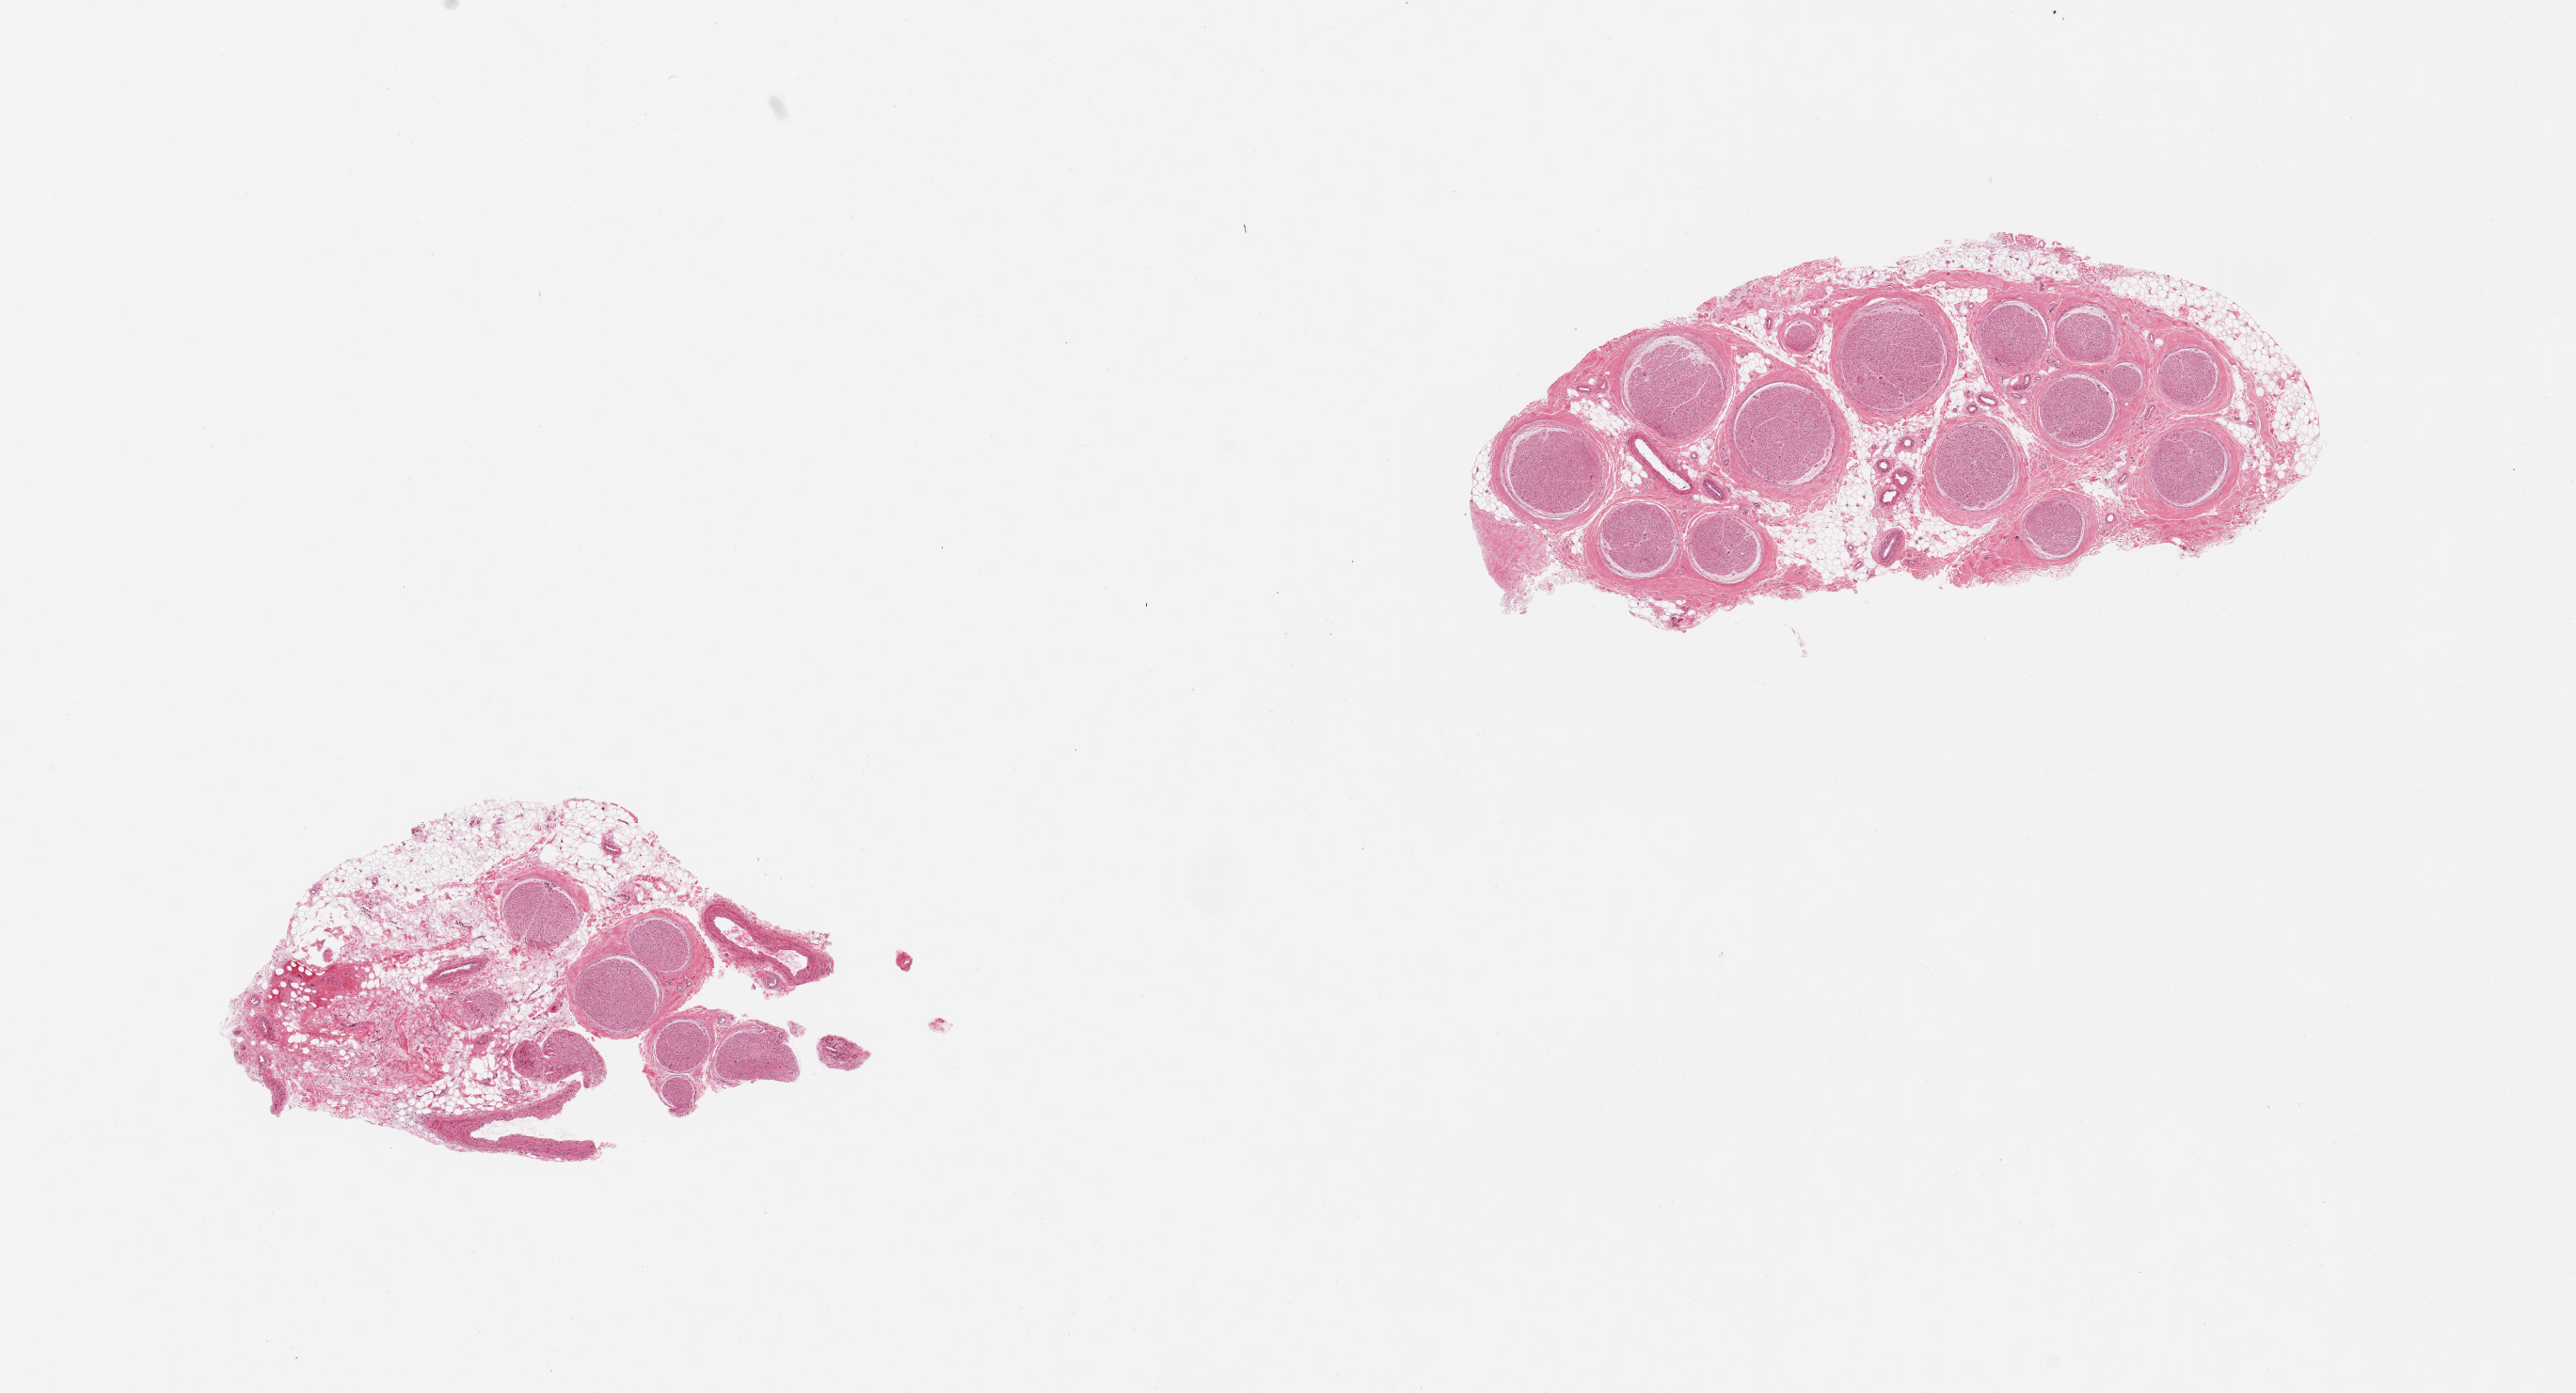
Hematoxylin and eosin (H&E) whole-slide image — whole scanned area (about 21.7 x 11.7 mm) shown as a low-resolution overview, PAXgene-fixed paraffin-embedded (PFPE) section, target tissue: tibial nerve, tissue donor sample. Donor sex: male.
Pathologist's review note for this sample: 2 pieces; one piece is 70% fat and vessels, second is 40% fat.